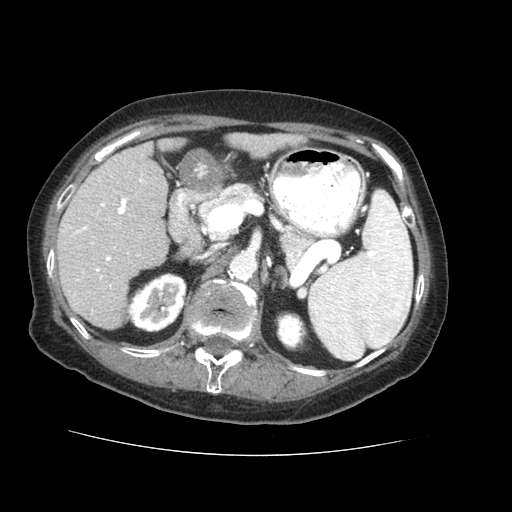
Contrast-enhanced abdominal CT (liver protocol), one axial slice; slice 26 of 73 in the series (ordered by position); reconstruction kernel STANDARD; 120 kVp; soft-tissue window (W 400 / L 40 HU); 2.5 mm slice thickness; 512 × 512 image matrix, field of view 360 × 360 mm. Case-level facts recorded for this patient, not image findings: diagnosis: hepatocellular carcinoma (patient treated with transarterial chemoembolisation; whether this scan precedes or follows treatment is not stated here); TNM stage (as recorded): Stage-IVB; Child-Pugh class: A.
Outlined on this slice (semi-automatic segmentation, software-assisted and operator-edited):
- liver parenchyma outside the tumour (the mass and vessels are separate outlines, so this box may not span the whole liver): bounding box (x1, y1, x2, y2) in pixels: (56, 134, 305, 328)
- liver vessels: (61, 173, 145, 287)